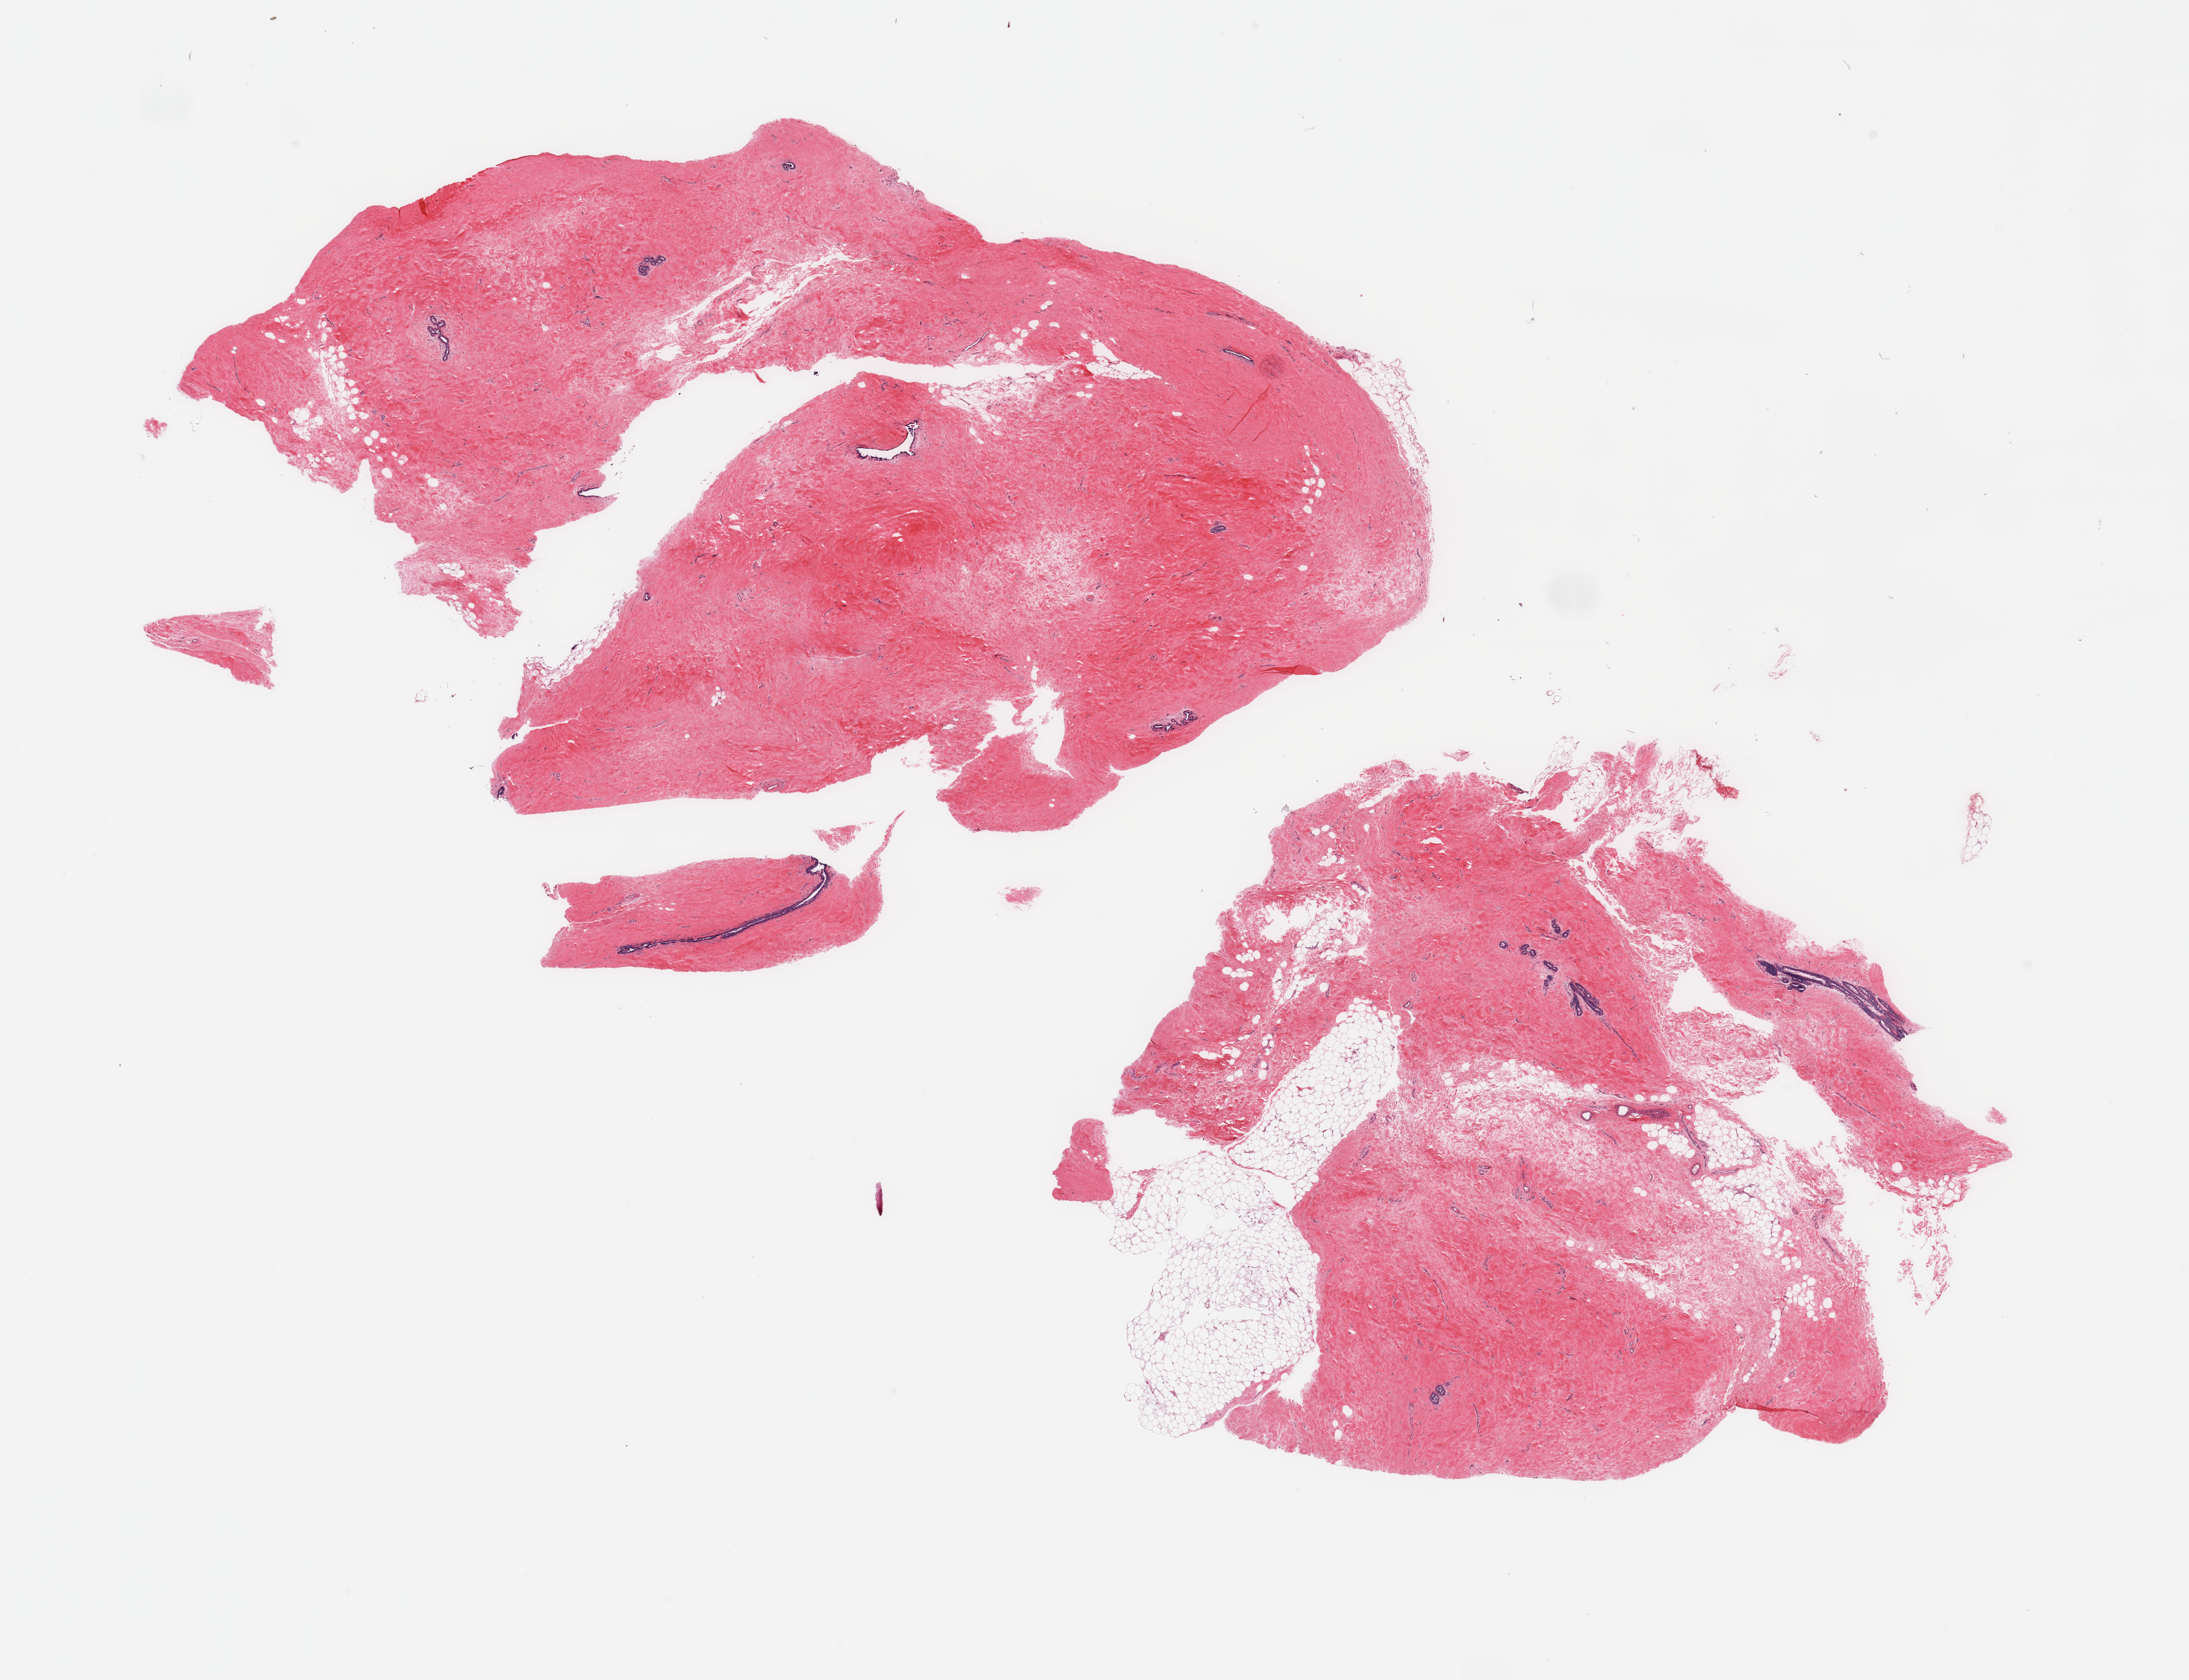
Digitized hematoxylin and eosin (H&E)-stained section, brightfield, a low-resolution overview of the entire scanned area, about 24.6 x 18.9 mm (from a 20x scan). PAXgene-fixed, paraffin-embedded tissue. Section of breast (target tissue). Tissue donor sample. Donor: male.
Review note (as recorded): 2 pieces; dense fibrous stroma with ductal structures suggestive of gynecomastoid stromal and ductal hyperplasia and adipose tissue.